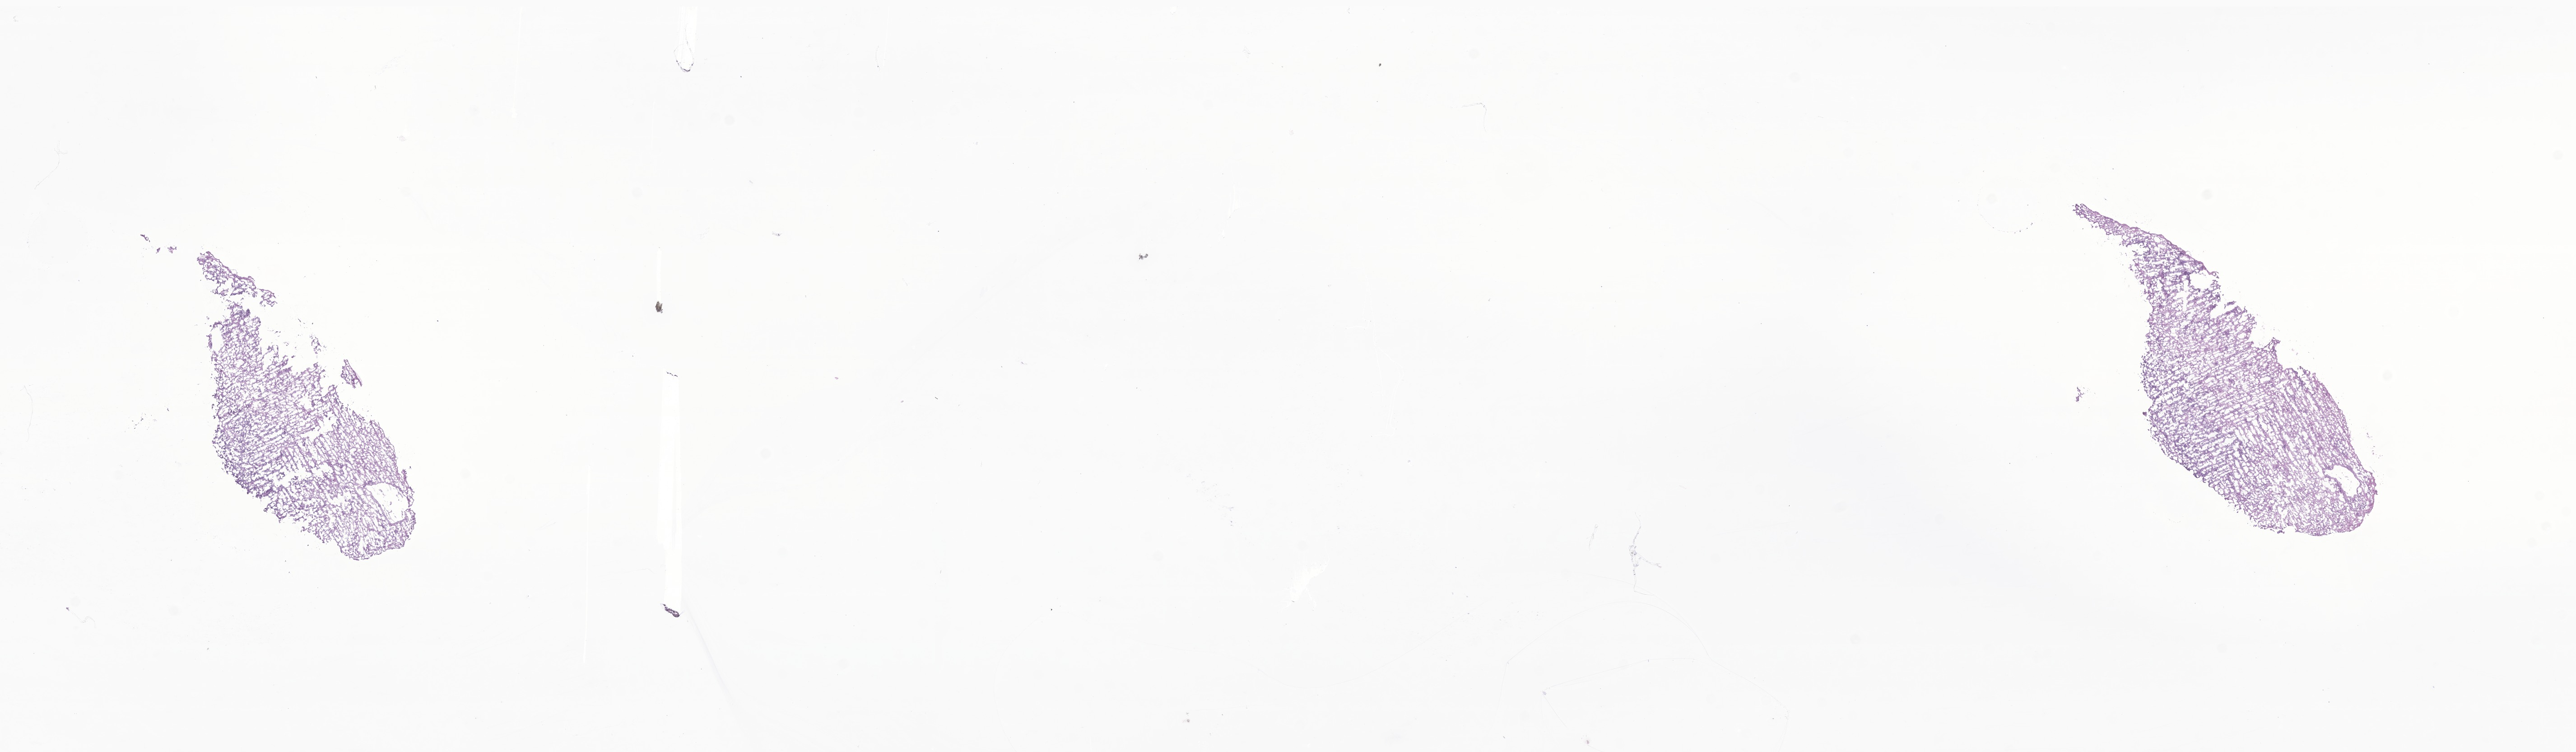
Digitized hematoxylin and eosin (H&E)-stained section of tumor tissue from the brain, low-resolution overview of the scanned area, about 24.1 x 7.0 mm; frozen section. Female patient, age 281 days.
- recorded diagnosis: Ependymoma, NOS